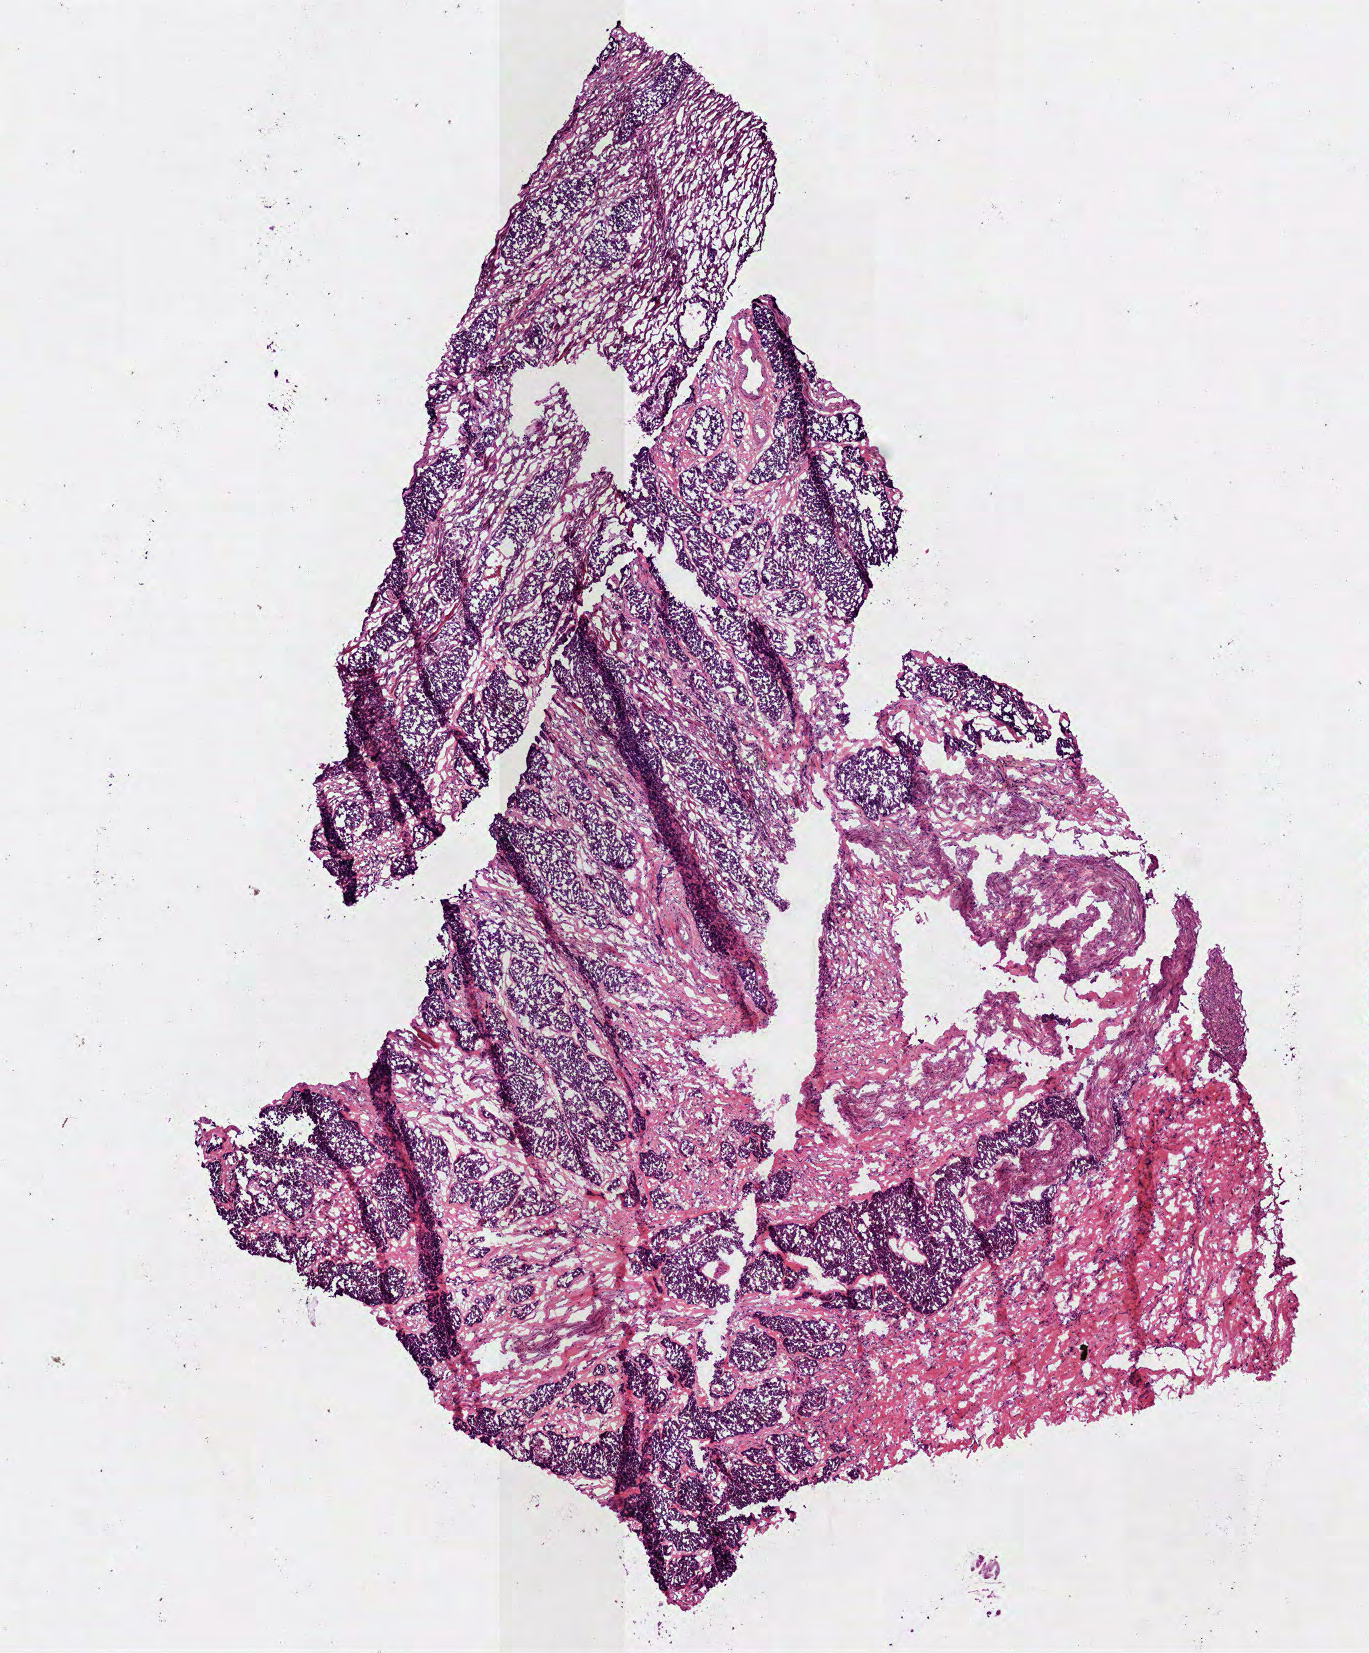
Digitized Hematoxylin and eosin (H&E) stained tissue section (whole slide) — whole scanned area (about 5.5 x 6.7 mm) shown as a low-resolution overview; frozen section; sample: primary tumour, head and neck. Male, age 60 years at initial diagnosis.
Diagnosis: Squamous cell carcinoma, NOS (tongue, NOS).